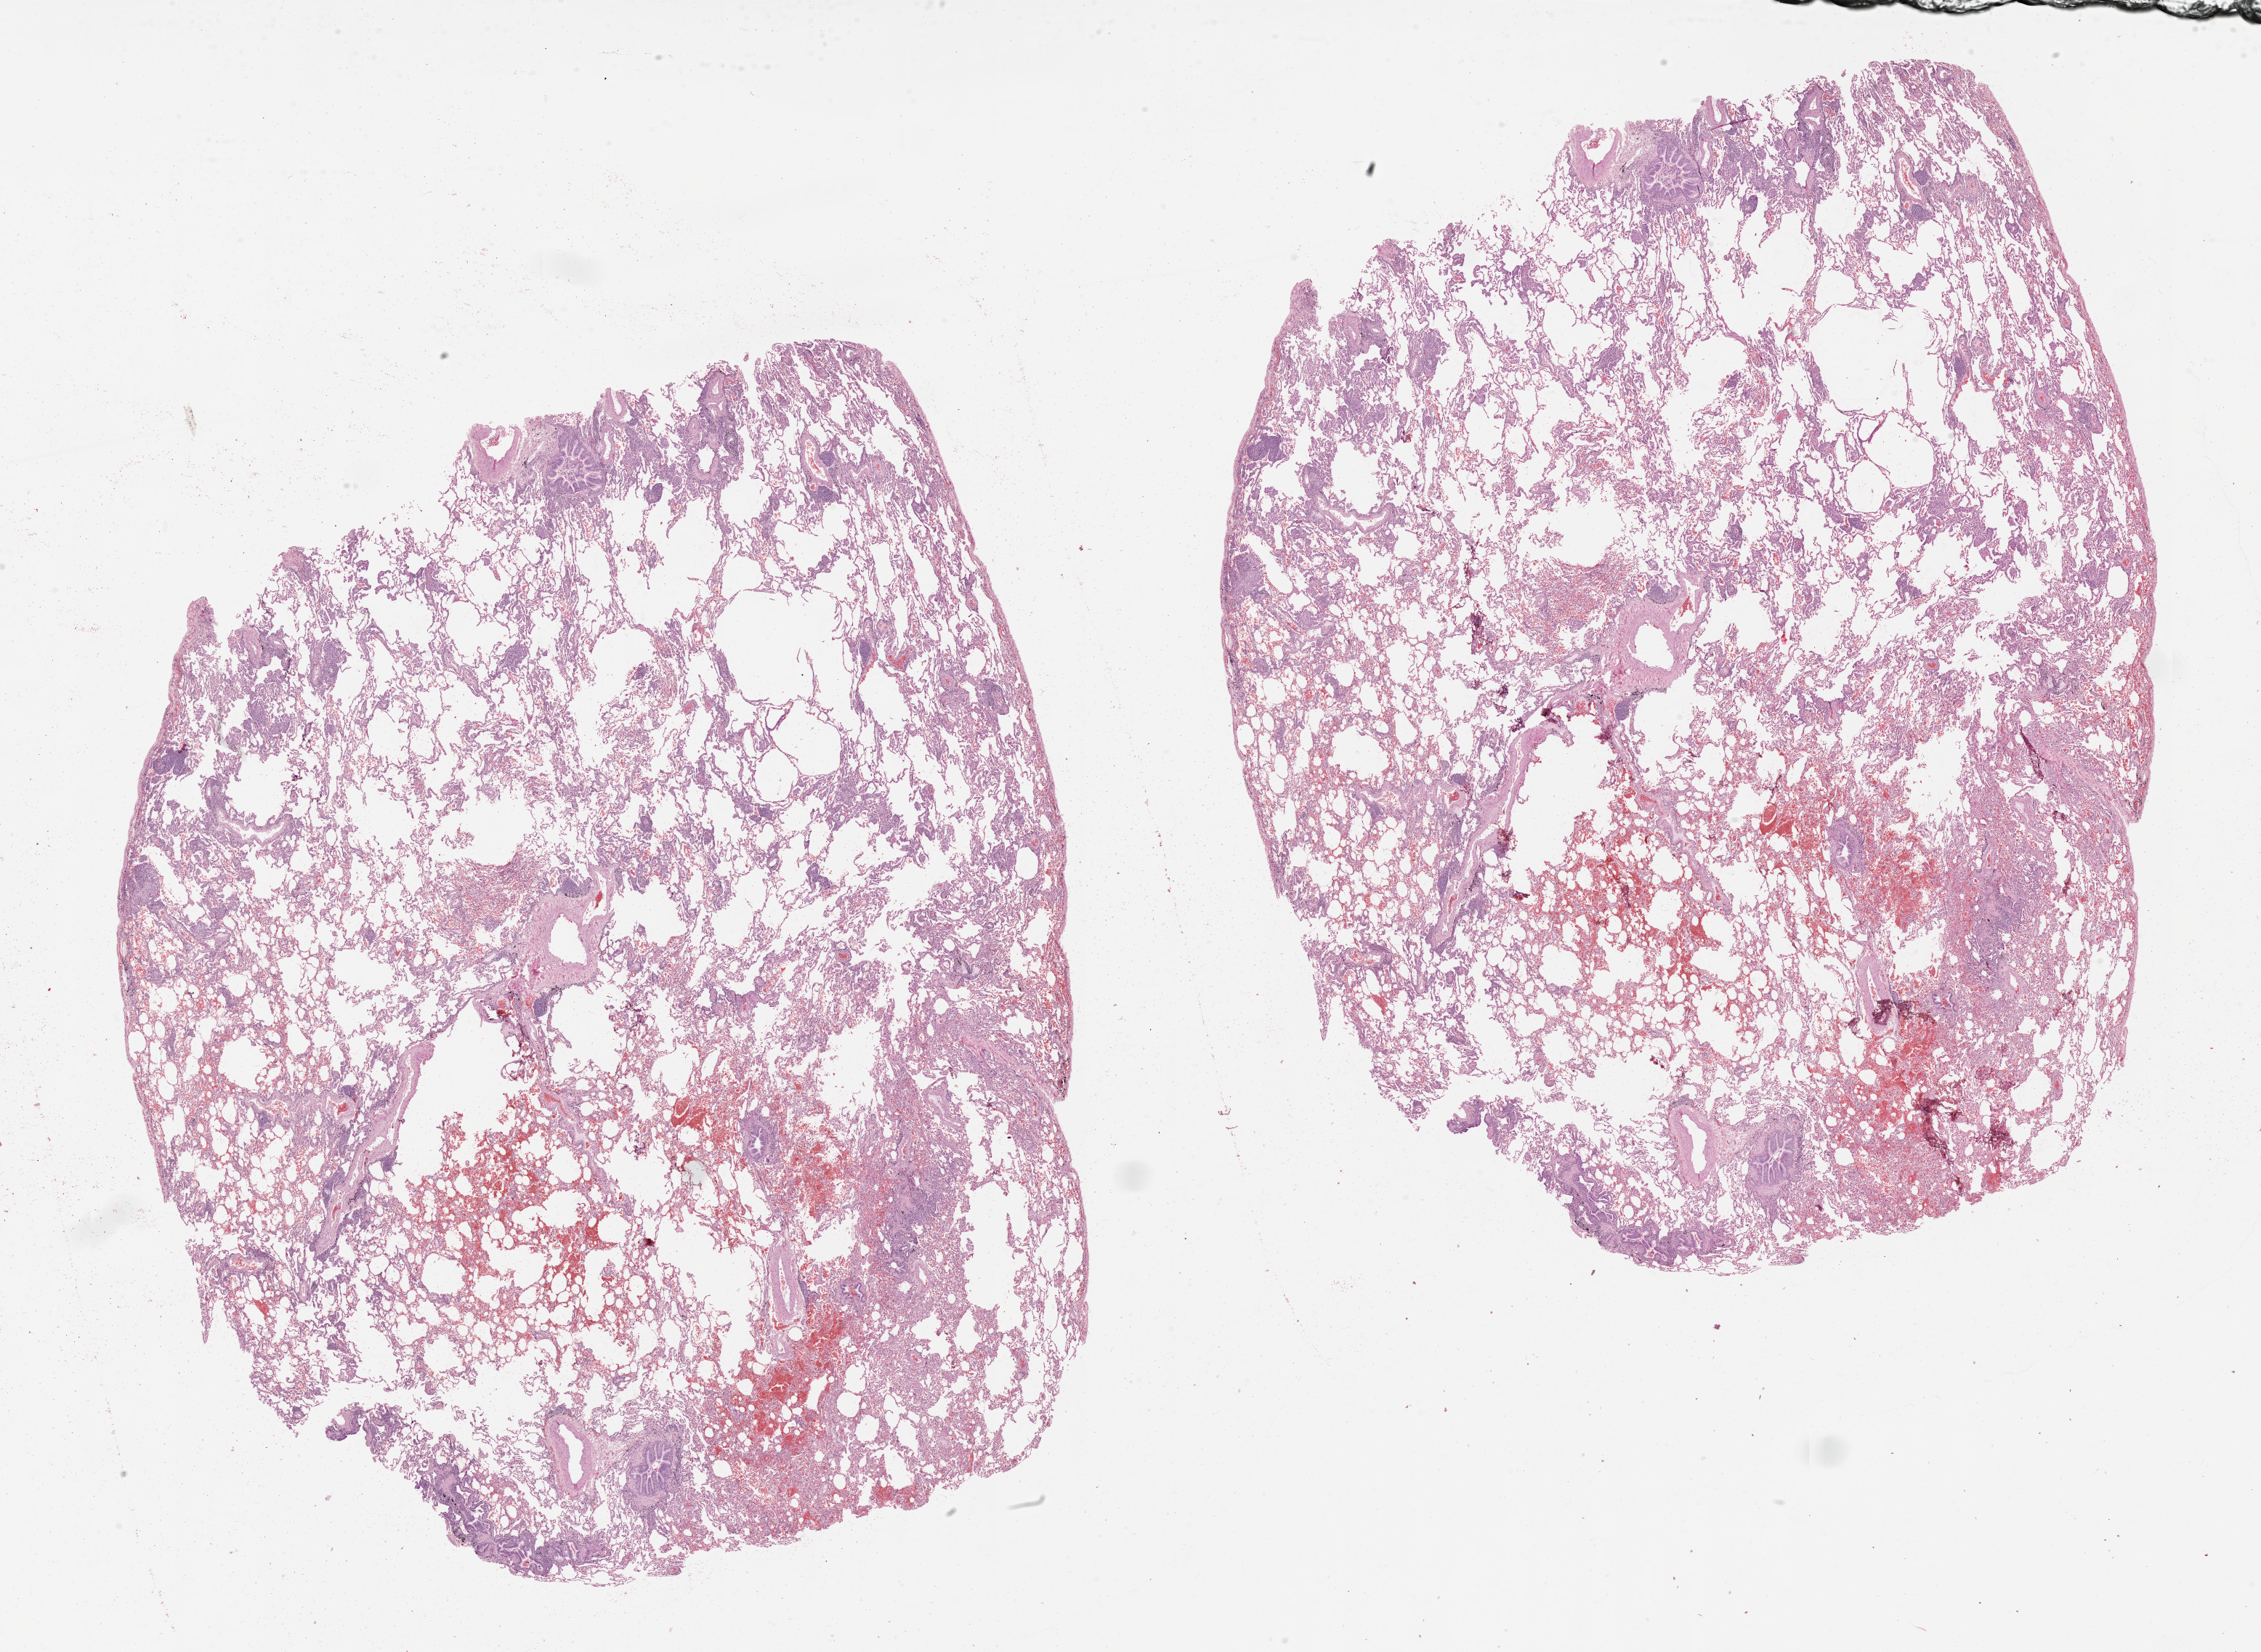
Whole-slide histology image, Hematoxylin and eosin (H&E) stained, whole scanned area (about 25.1 x 18.3 mm) shown as a low-resolution overview. Lung, normal (non-tumour) tissue. Male, 69 y/o.
• this section: normal (non-tumour) tissue from the same patient
• patient diagnosis (cohort enrolment): squamous cell carcinoma (lung)